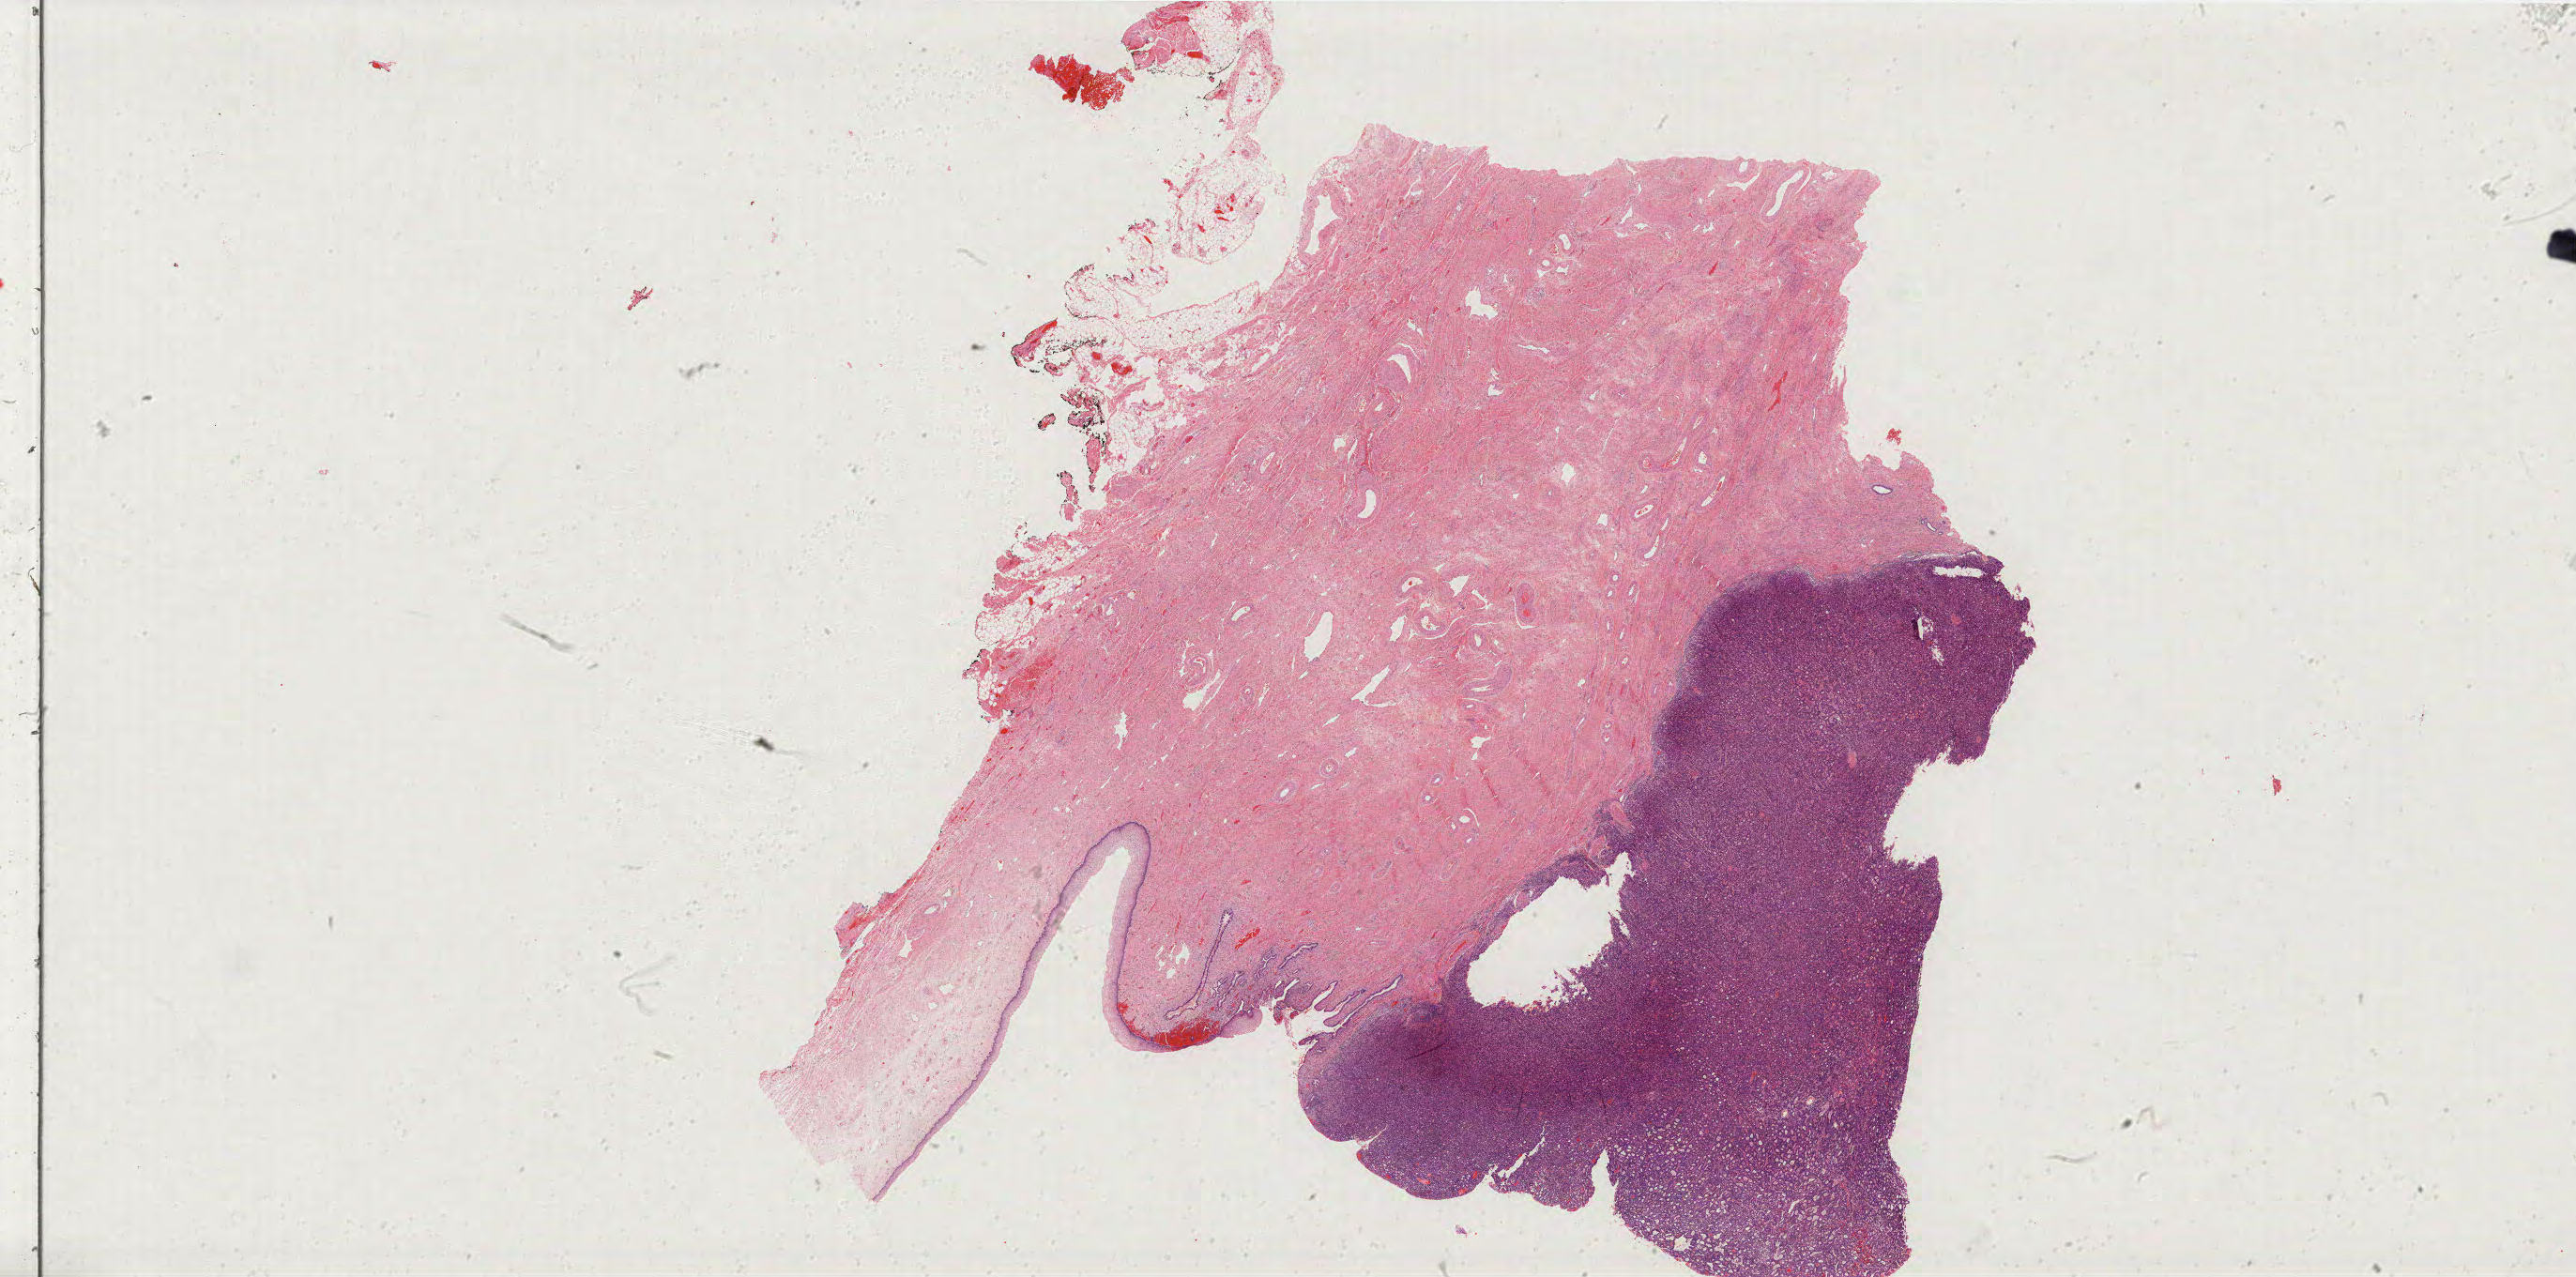
Whole-slide histology image, H&E — shown as a low-resolution overview of the whole scanned area (about 43.9 x 21.8 mm). Formalin-fixed paraffin-embedded (FFPE) diagnostic section. Cervix, primary tumour sample. Patient: female, age at initial diagnosis 40 years. Histologic grade: G3 (poorly differentiated).
Histologic diagnosis: Adenocarcinoma, endocervical type (cervix uteri). Lymph nodes positive (case pathology): 0 of 14 examined. FIGO stage: IB1.